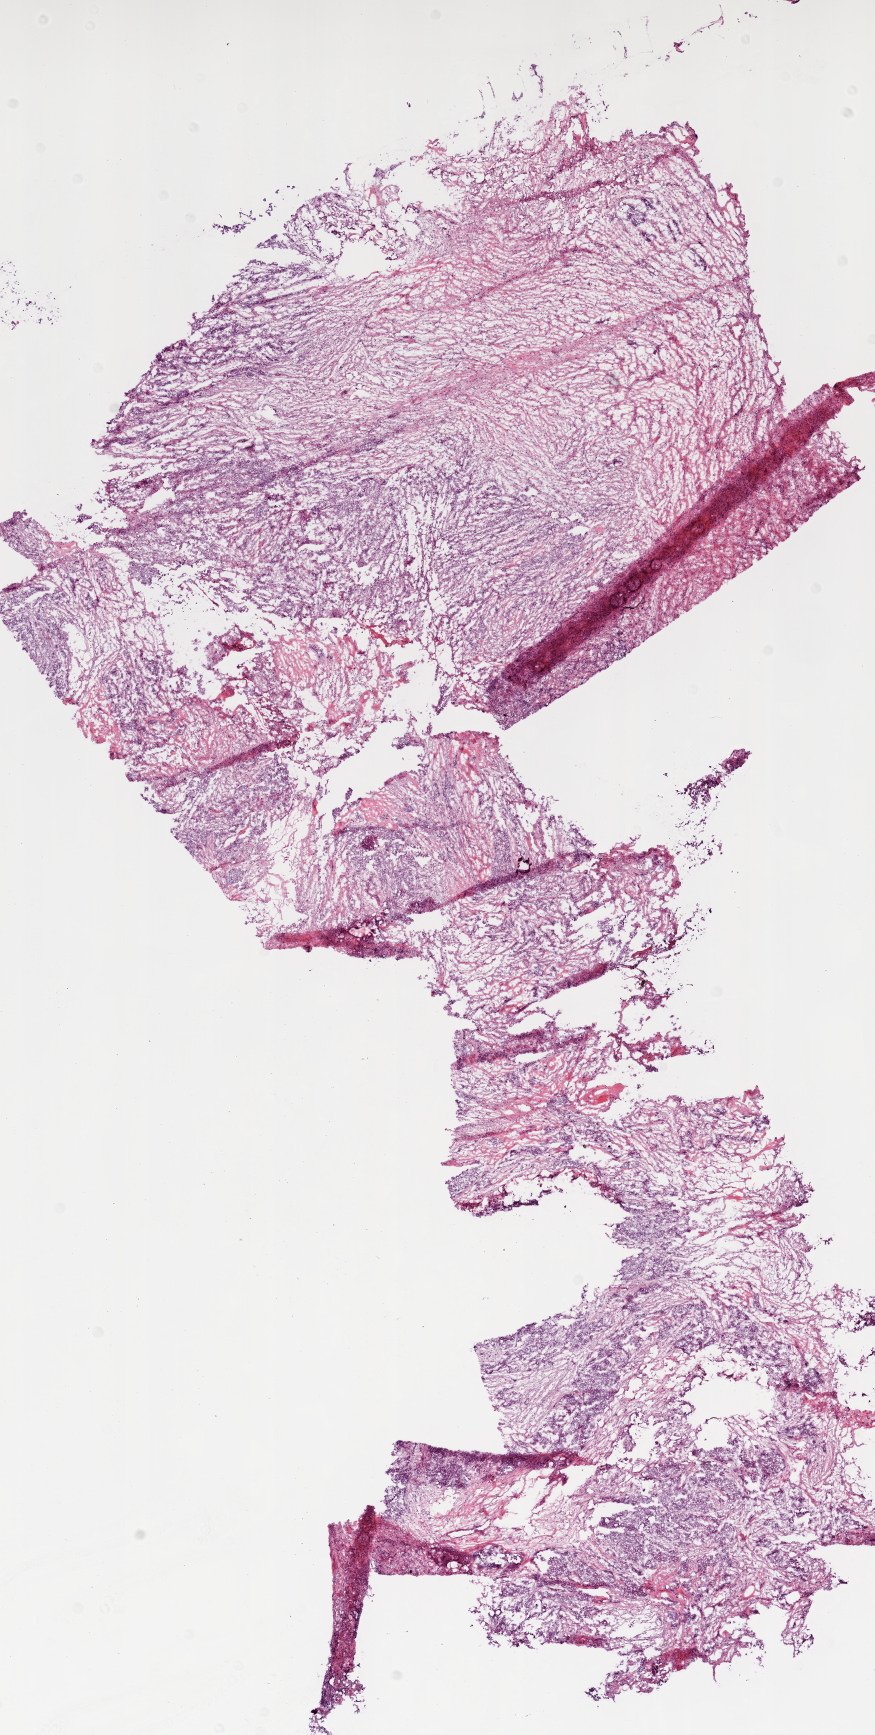
Digitized H&E tissue section (whole slide), shown as a low-resolution overview of the whole scanned area (about 7.0 x 13.9 mm, from a 20x scan); frozen section from the bottom of the tissue portion; primary tumour sample from the ovary. Female, age 46 years at initial diagnosis. Histologic grade: G3 (poorly differentiated). Slide review estimates, as recorded: tumour cells 60%, tumour nuclei 70%, normal cells 0%, stromal cells 40%, necrosis 0%.
- pathologic diagnosis: Serous cystadenocarcinoma, NOS
- laterality: bilateral
- FIGO stage: IIIC